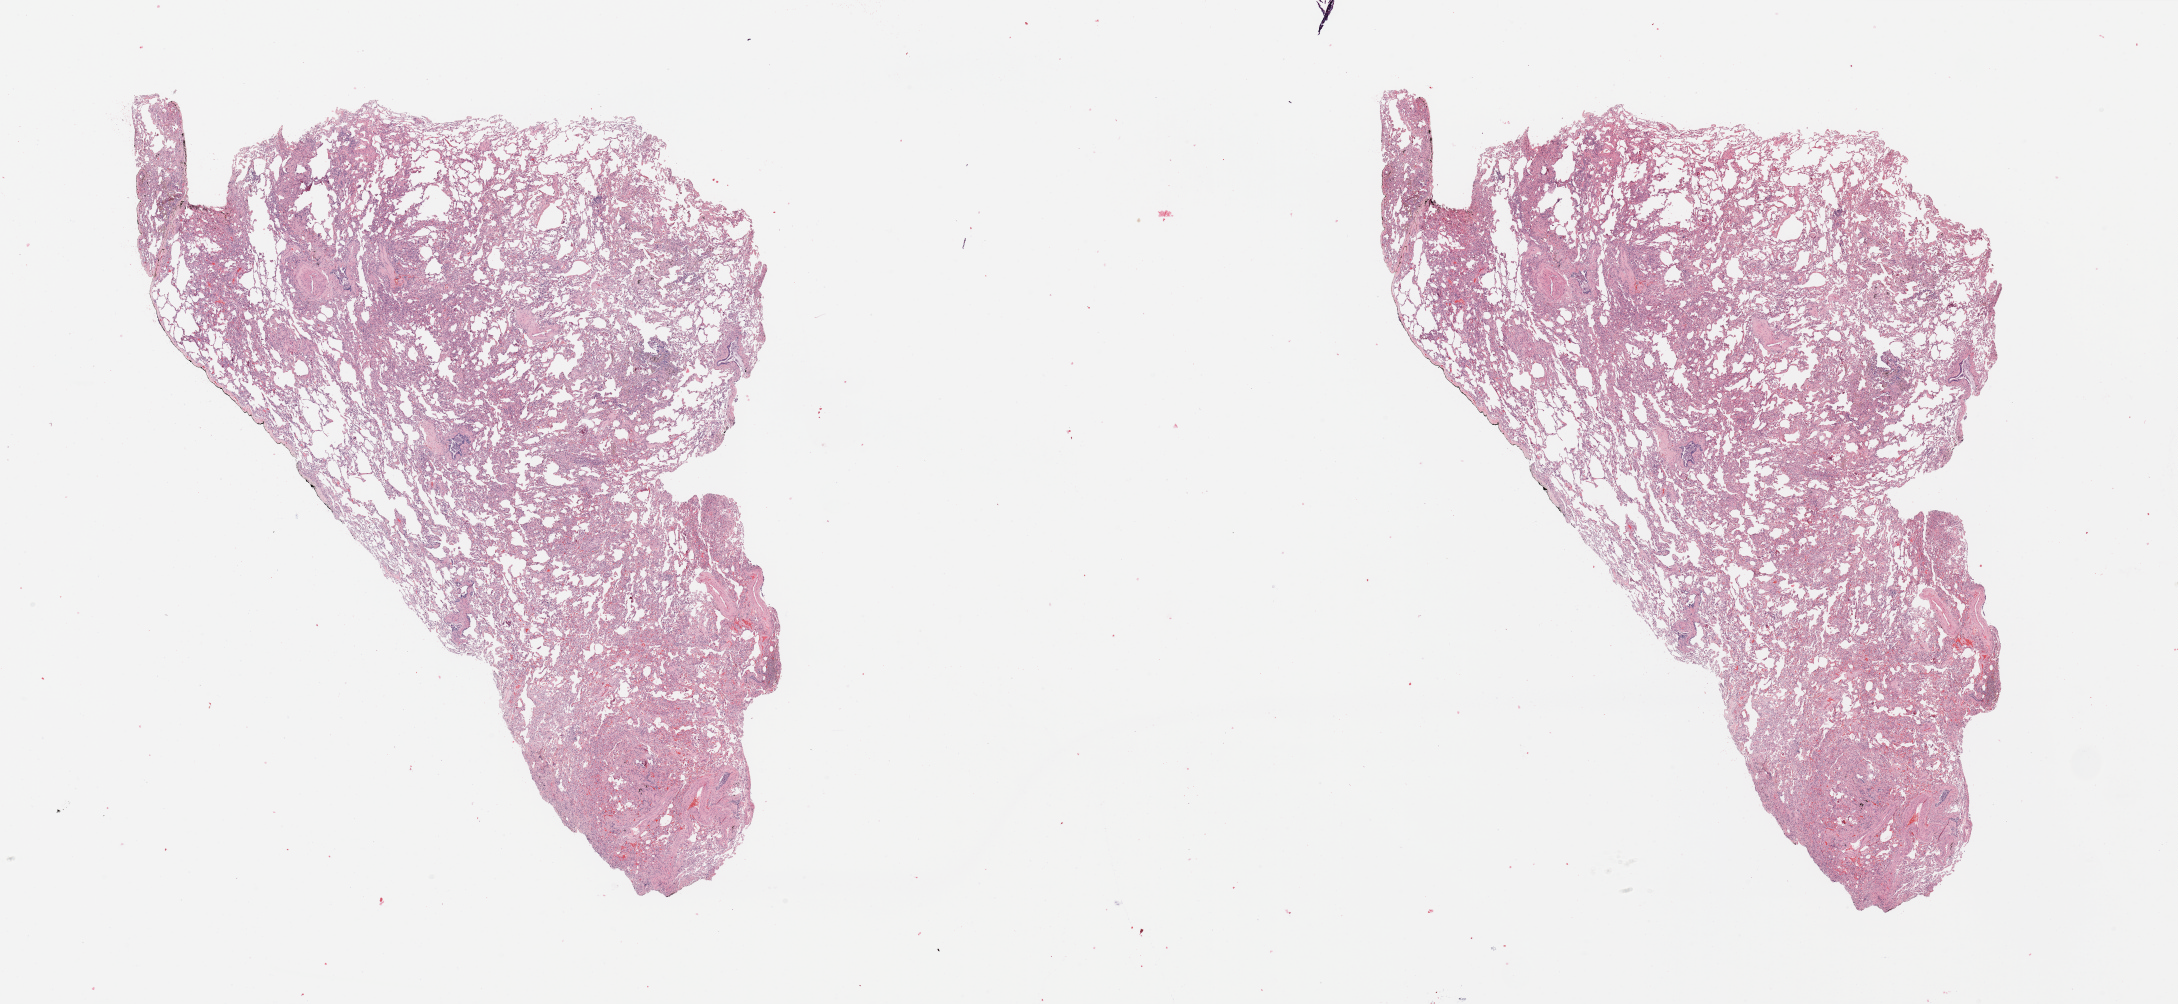
Whole-slide histology image, H&E, whole scanned area (about 34.5 x 15.9 mm) shown as a low-resolution overview. Normal (non-tumour) tissue sample, sampled site: lung. Female, 68 y/o.
This section: normal (non-tumour) tissue from the same patient. Patient diagnosis: Adenocarcinoma, NOS.